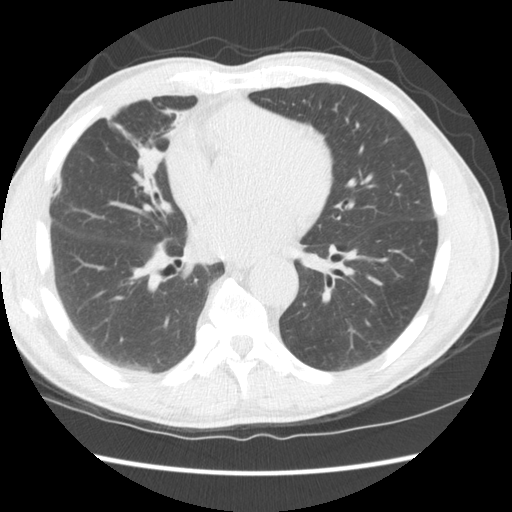
Low-dose screening chest CT, one axial slice. Slice 65 of 147 in the series (ordered by position). Reconstruction kernel STANDARD. 120 kVp. Lung window (W 1500 / L -600 HU). 2.5 mm slice thickness. 512 × 512 image matrix.
Outlined on this slice (manually delineated by an expert):
- lesion 1 (tumor, middle lobe of right lung): bounding box [x1, y1, x2, y2] px = [141, 147, 163, 172]